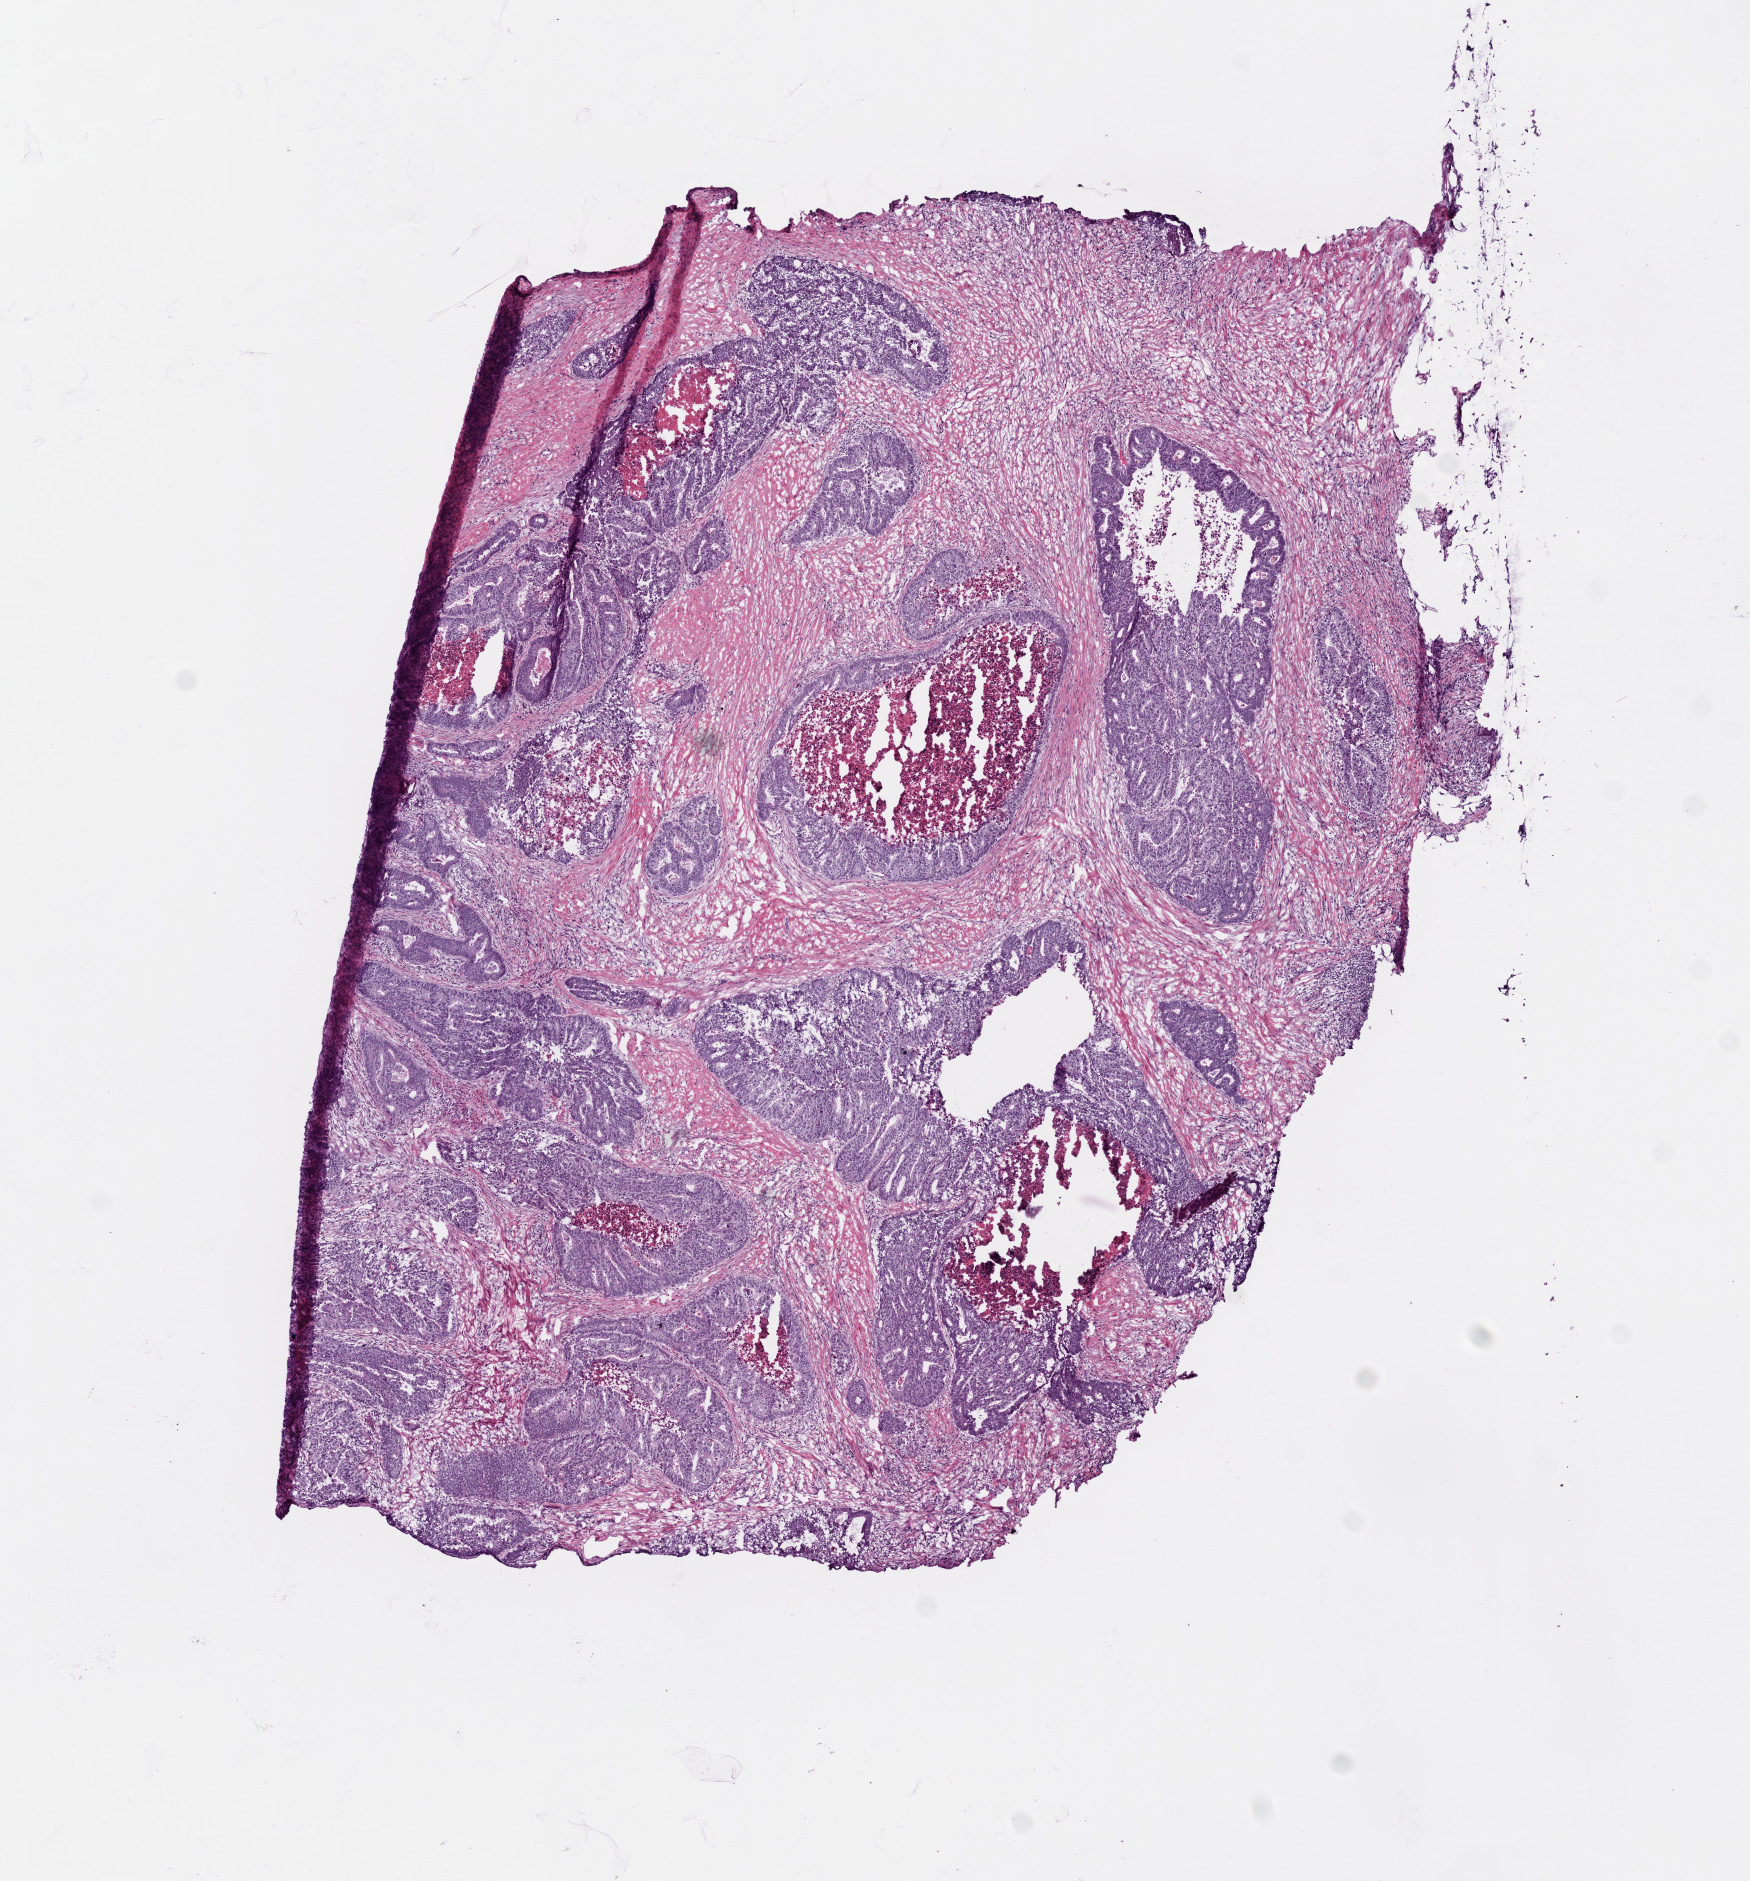
Hematoxylin and eosin (H&E) stained whole-slide image — whole scanned area (about 7.0 x 7.5 mm) shown as a low-resolution overview, frozen section from the top of the tissue portion, primary tumour sample from the colon. Patient: male, age at initial diagnosis 63 years.
Pathologic diagnosis: Adenocarcinoma, NOS.